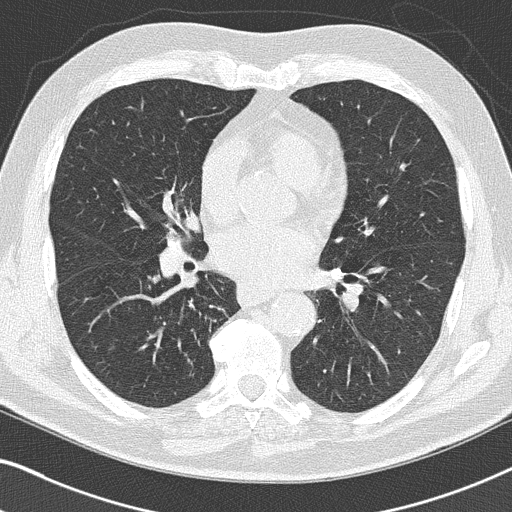
Low-dose screening chest CT, axial slice. Third screening round (two years after baseline). Lung window (W 1500 / L -600 HU). Male participant, aged 66 years at enrolment. Current smoker at enrolment.
• Expert reader's lesion annotation, box from (x=141, y=262) to (x=231, y=325) px.
• Reader record for this screening exam (exam-level; its link to the box is not recorded): non-calcified nodule or mass ≥4 mm, right upper lobe, 5 × 4 mm, smooth margins, pre-existing on the prior screen: yes; interval growth: no.
• Lung cancer was diagnosed 38 days after this screen: squamous cell carcinoma, NOS, right lower lobe, poorly differentiated (G3), stage IIA (AJCC 6th edition), 22 mm at pathology.